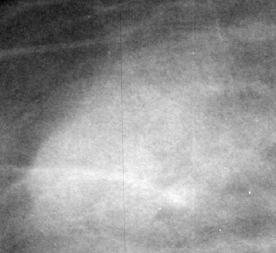
Cropped region of a digitized screen-film mammogram centred on a radiologist-marked abnormality; right breast; CC view; BI-RADS breast density category 2 (scale 1–4).
Marked abnormality: mass, shape asymmetric breast tissue; BI-RADS assessment category 2; subtlety rating 4 on a 1 (subtle) to 5 (obvious) scale; benign without callback (not worked up further).